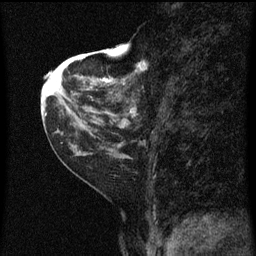
Breast MRI (dynamic contrast-enhanced), one sagittal slice; slice 23 of 60 in the series (ordered by position); dynamic contrast-enhanced series, image 2 of 3 at this slice position (ordered by acquisition); 1.5 T; TE 4.2 ms, TR 8 ms; 2 mm slice thickness; 256 × 256 image matrix, field of view 180 × 180 mm. Female patient, age 48 years.
Outlined on this slice (semi-automatically segmented with operator editing):
- analysis volume of interest (the breast-tissue region the enhancement analysis was run in; not a lesion): bounding box (x1, y1, x2, y2) in pixels: (128, 58, 175, 125)
- tumour enhancement mask (voxels above the 70 % enhancement threshold inside the analysis volume of interest): (129, 60, 148, 119)